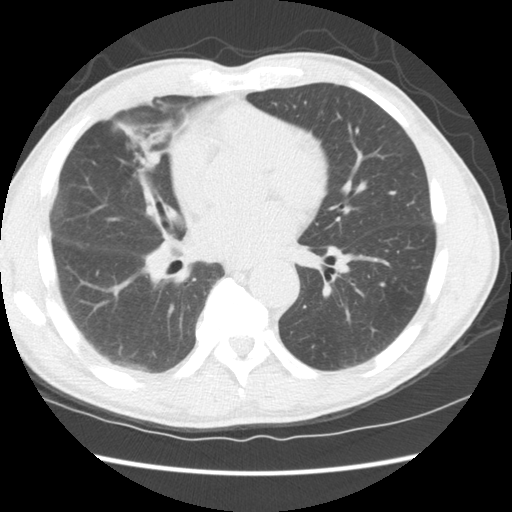
Chest CT (low-dose screening protocol), one axial image; third screening round (two years after baseline); lung window (W 1500 / L -600 HU); 2.5 mm slice thickness; 120 kVp; slice 67 of 147 in the series. Male participant, aged 65 years at enrolment. Current smoker at enrolment.
• Lesion marked by an expert reader, box from (x=103, y=128) to (x=176, y=211) px.
• Screening reader's record for this exam (one nodule recorded; not confirmed to be the boxed lesion): non-calcified nodule or mass ≥4 mm, right middle lobe, 16 × 15 mm, smooth margins, soft tissue attenuation, pre-existing on the prior screen: yes; interval growth: yes.
• Official screen result: positive, other.
• Lung cancer was diagnosed 357 days after this screen: squamous cell carcinoma, NOS, right middle lobe, poorly differentiated (G3), stage IA (AJCC 6th edition), 23 mm at pathology.